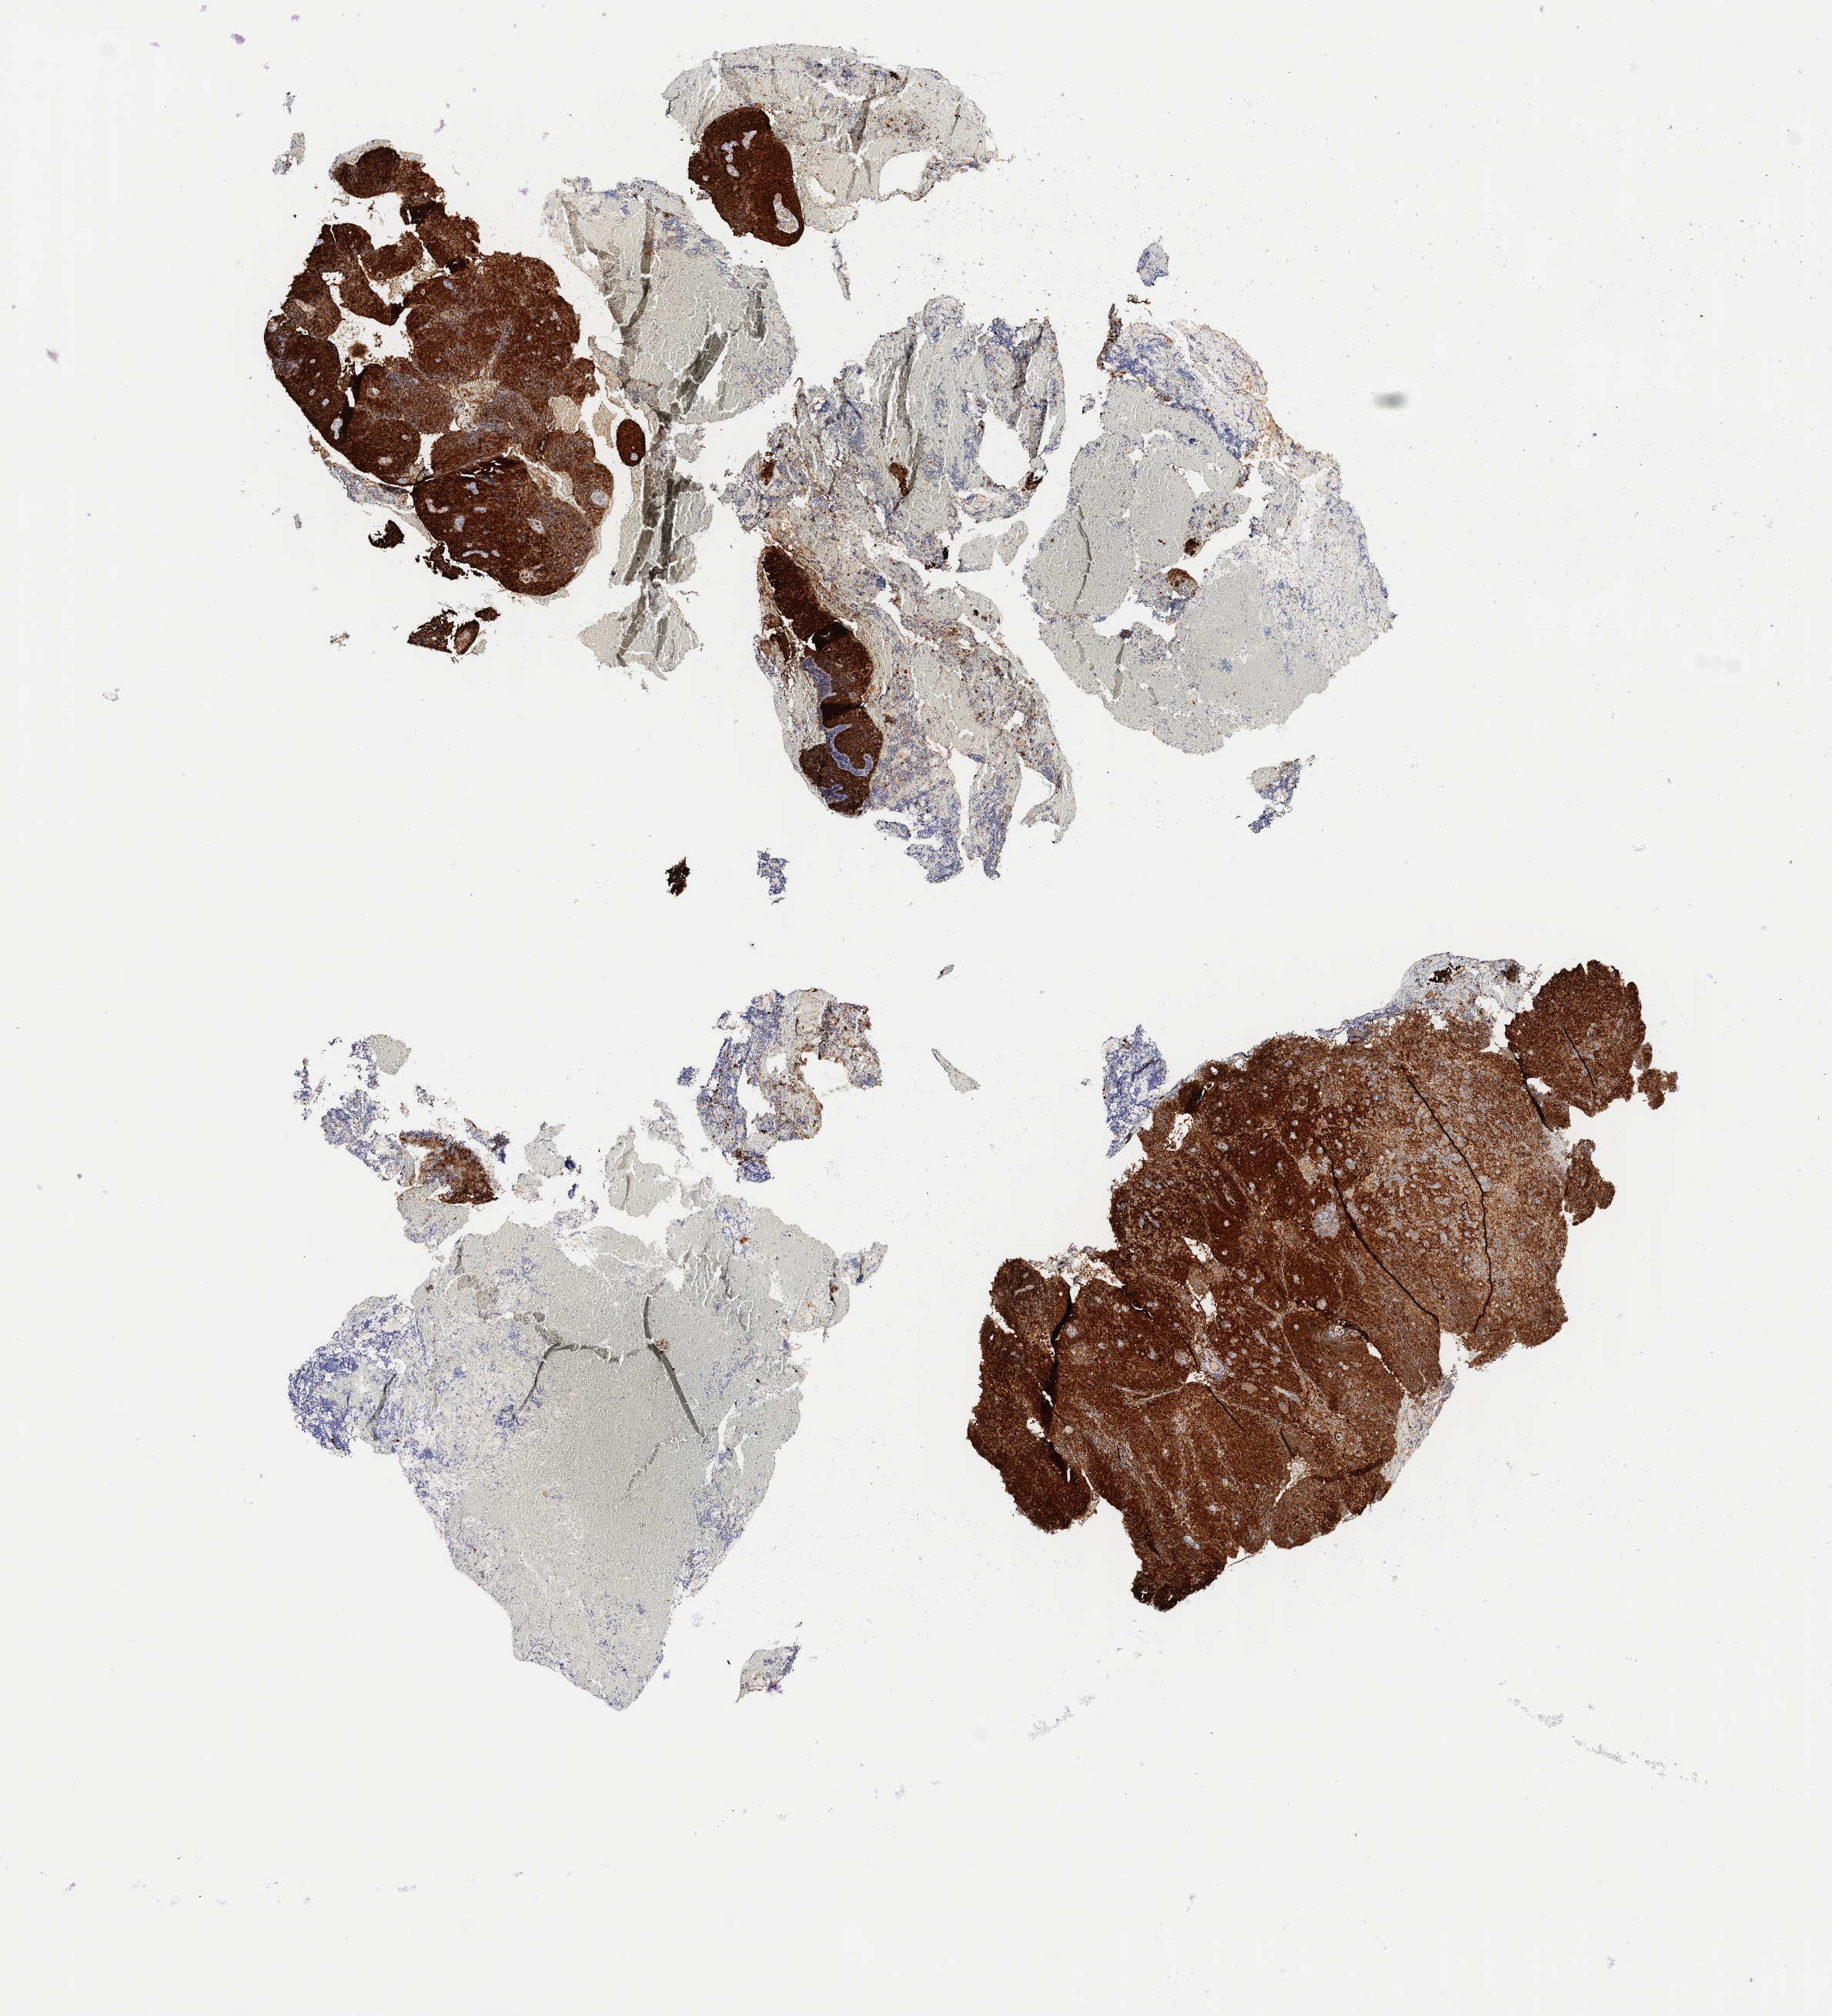
IHC for p16 (p16INK4a), whole-slide image, whole scanned area (about 9.5 x 10.4 mm) shown as a low-resolution overview. Specimen: tumor tissue. Site: cervix. Patient: female, aged 59.
Histologic diagnosis: Squamous cell carcinoma, large cell, nonkeratinizing, NOS.